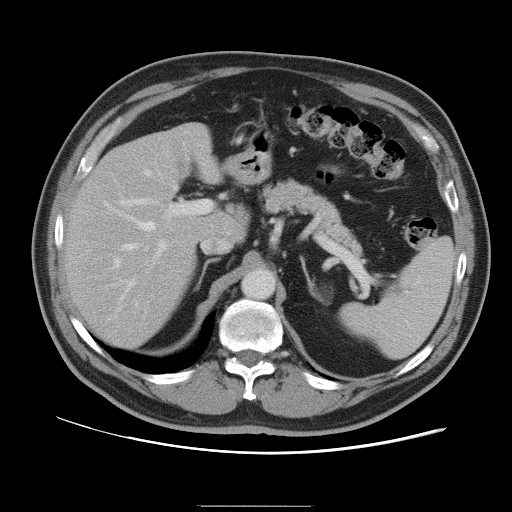
Contrast-enhanced abdominal CT, one axial slice; slice 63 of 105 in the series (ordered by position); 120 kVp; soft-tissue window (W 400 / L 40 HU); 5 mm slice thickness; 512 × 512 image matrix, field of view 399 × 399 mm. Male patient, age 64 years. From the clinical record (not read from this slice): diagnosis: colorectal cancer liver metastases, imaged before liver resection; multiple liver metastases: yes; largest metastasis: 3 cm.
Outlined on this slice (expert manual segmentation):
- hepatic veins: bounding box (x1, y1, x2, y2) in pixels: (121, 172, 155, 286)
- liver: (65, 124, 244, 347)
- planned liver remnant (the part of the liver to remain after resection): (65, 136, 244, 348)
- portal vein (with intrahepatic branches): (114, 199, 212, 313)